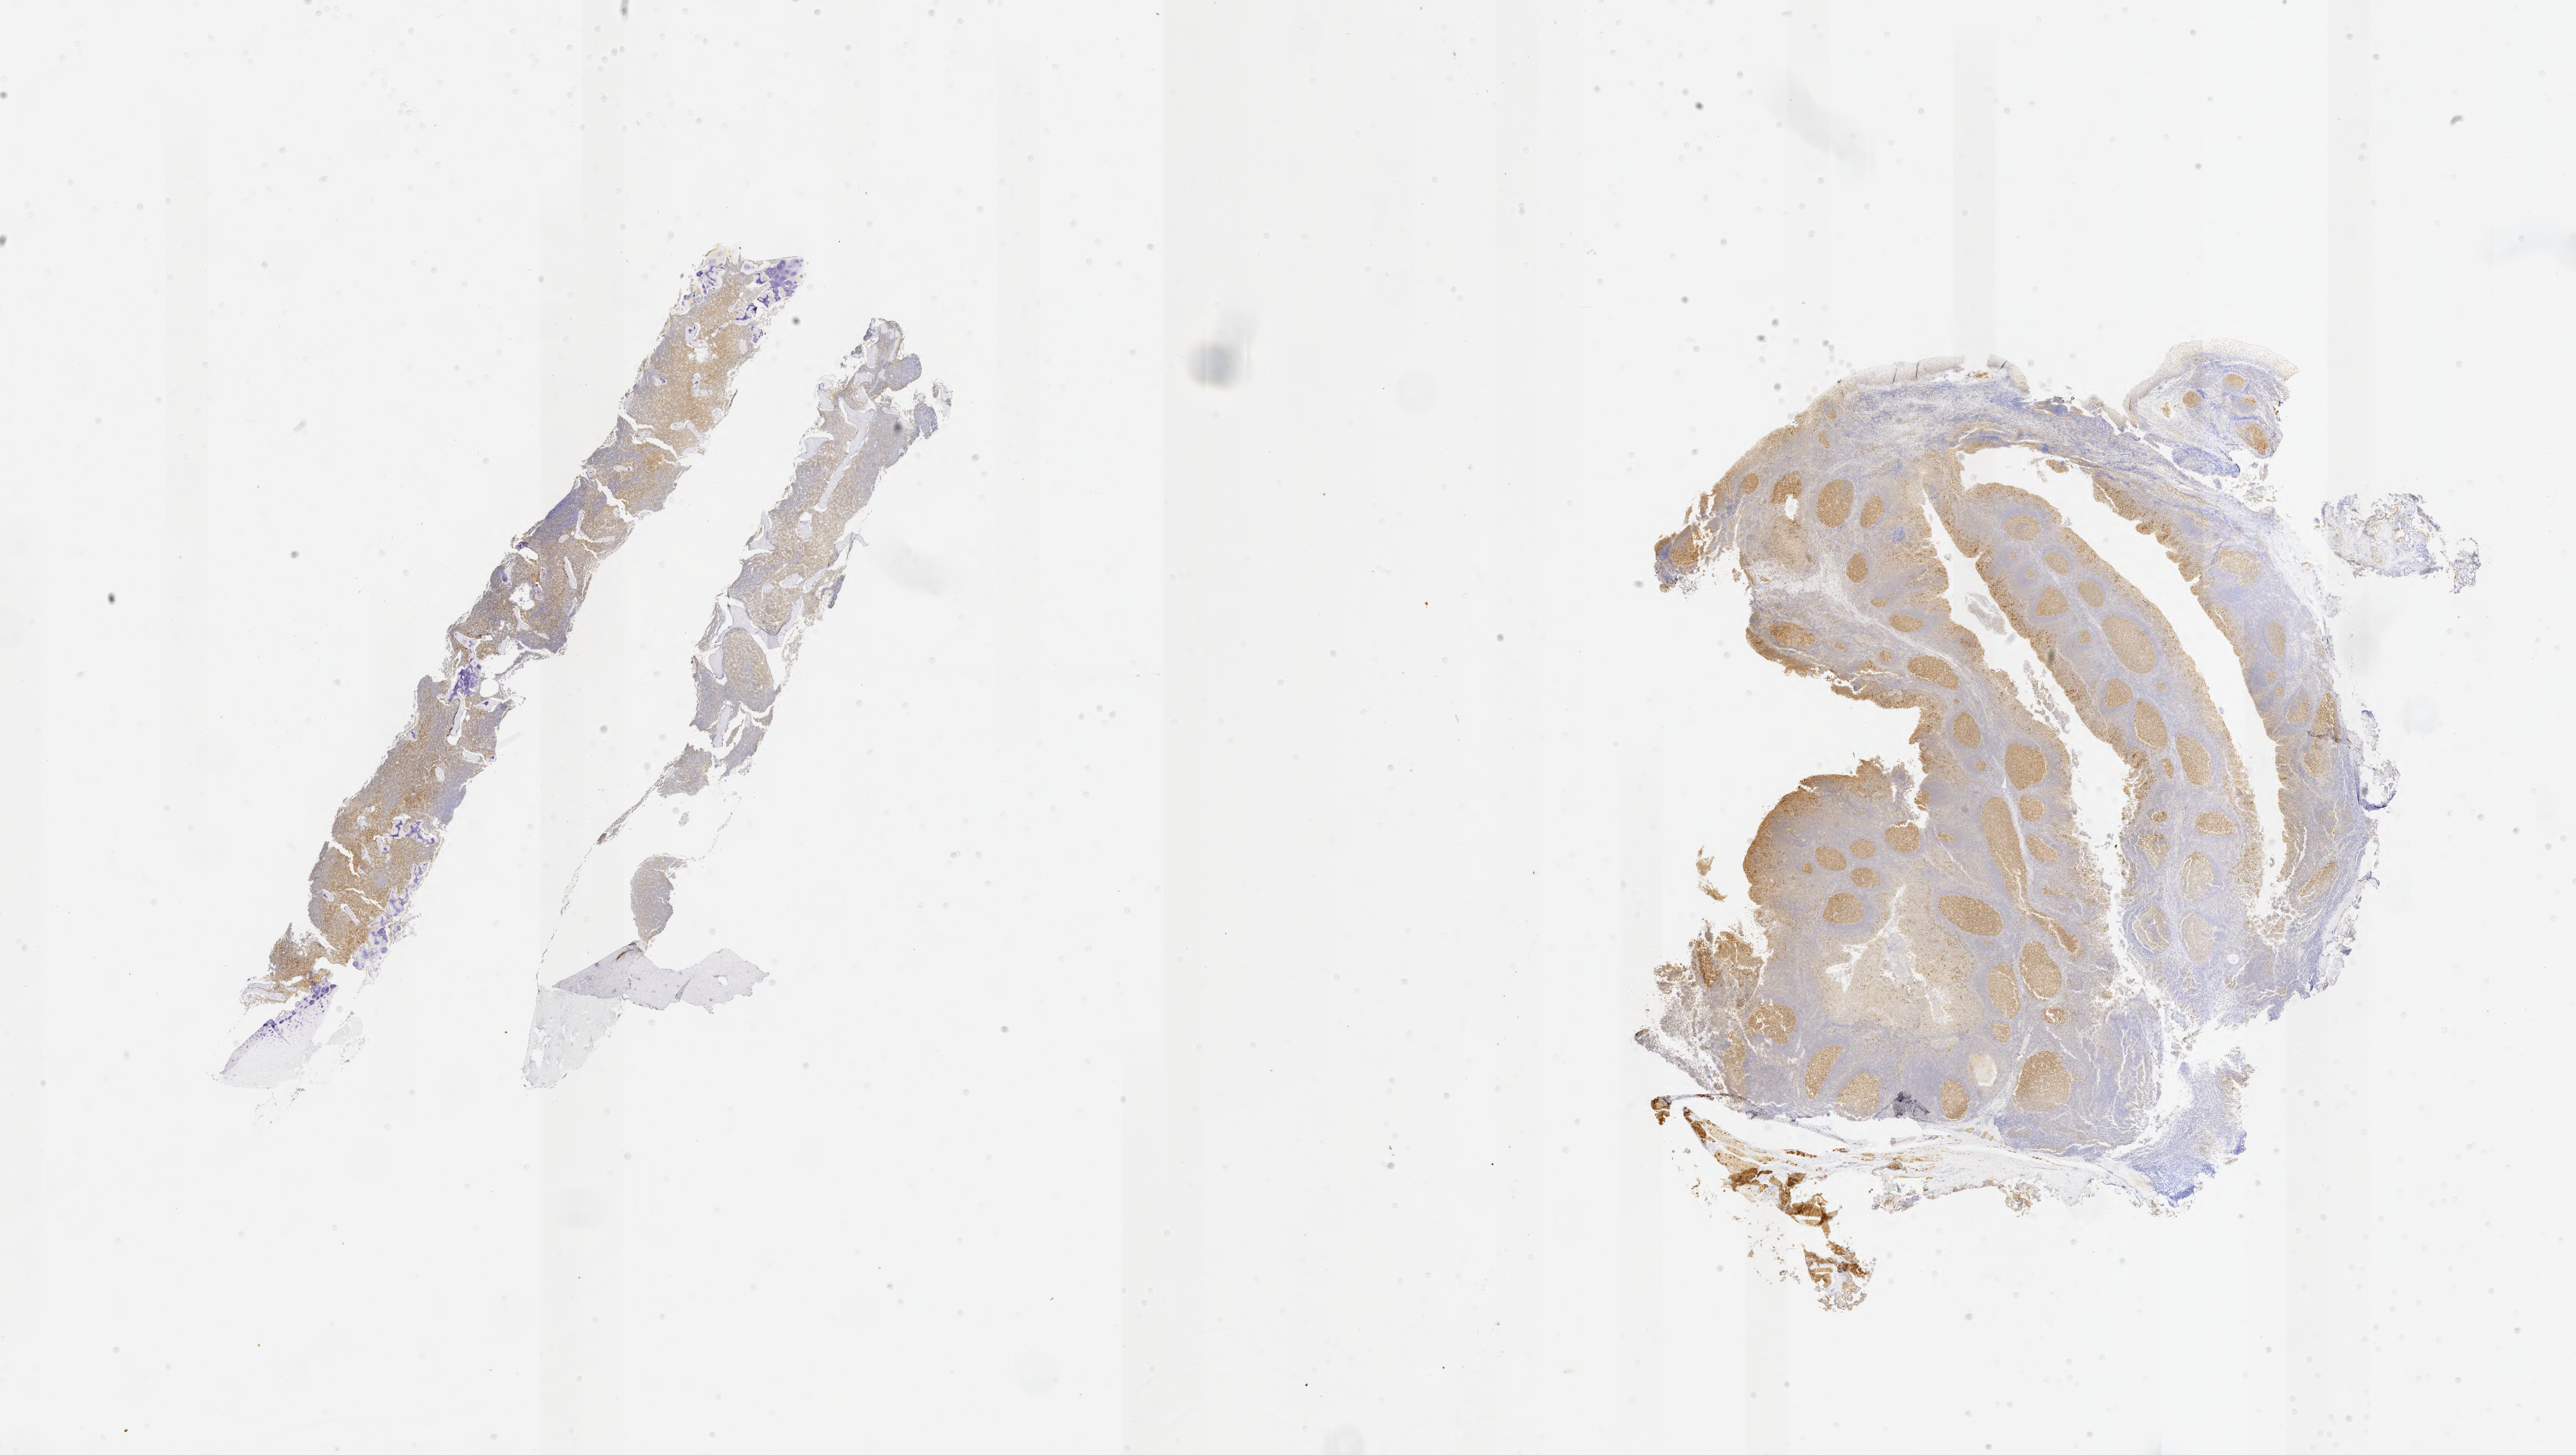
Immunohistochemistry (IHC) whole-slide image stained for BCL6, shown as a low-resolution overview of the whole scanned area (about 31.2 x 17.6 mm), tumor tissue, anatomic site: bone marrow. Male patient, age 16 years.
Histologic diagnosis: Burkitt lymphoma, NOS.